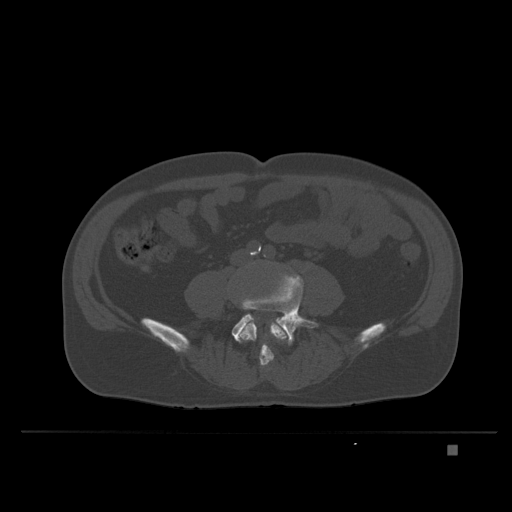
CT including the spine, one axial slice; slice 65 of 435 in the series (ordered by position); bone window (W 1800 / L 400 HU); 1.5 mm slice thickness; 512 × 512 image matrix. Male patient, age 73 years. Case-level facts recorded for this patient, not image findings: primary cancer: skin.
Structures marked on this image (semi-automatically segmented with operator editing):
- L4 vertebra: bounding box [x1, y1, x2, y2] px = [238, 318, 288, 370]
- L5 vertebra: [232, 276, 319, 346]